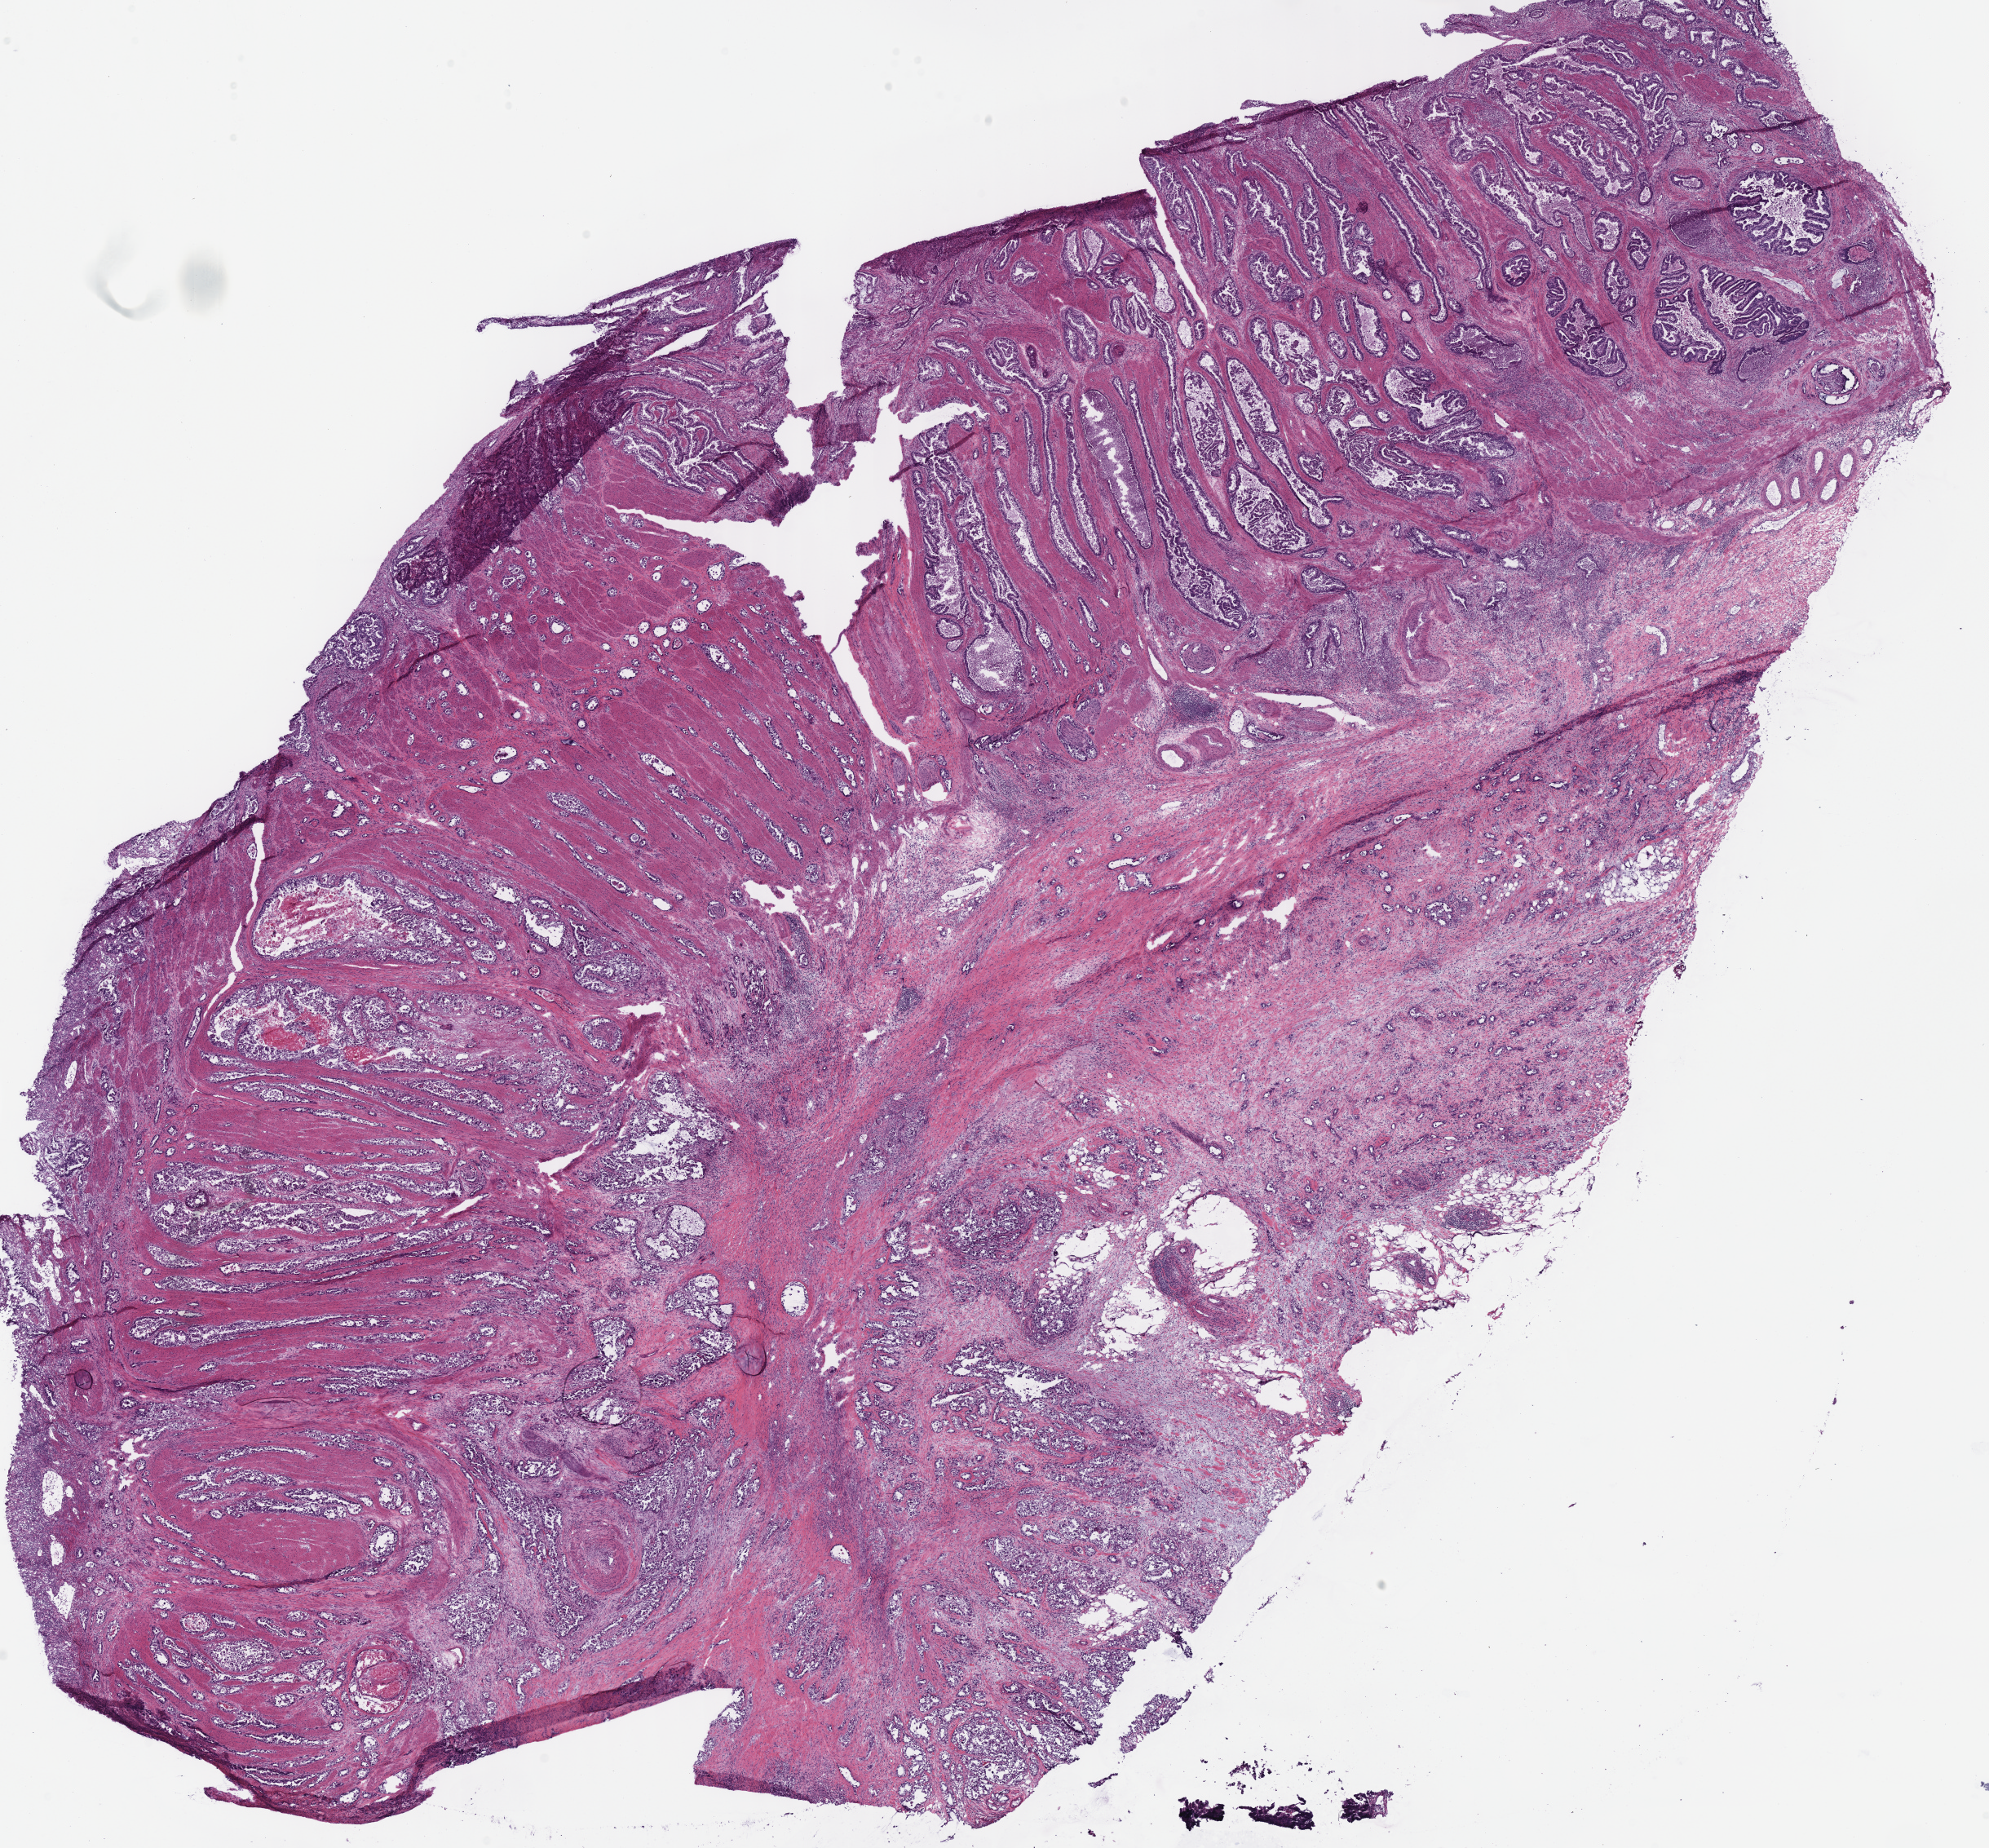
Whole-slide histology image, H&E, shown as a low-resolution overview of the whole scanned area (about 19.2 x 17.9 mm), frozen section from the top of the tissue portion, stomach, primary tumour sample. Male, age 74 years at initial diagnosis. Histologic grade: G2 (moderately differentiated). Pathologist review of this section (percent, as recorded): tumour cells 50%, tumour nuclei 60%, normal cells 0%, stromal cells 50%, necrosis 0%.
Pathologic diagnosis: Adenocarcinoma, NOS. Lymph nodes positive (case pathology): 2 of 15 examined. AJCC pathologic stage: IIB.